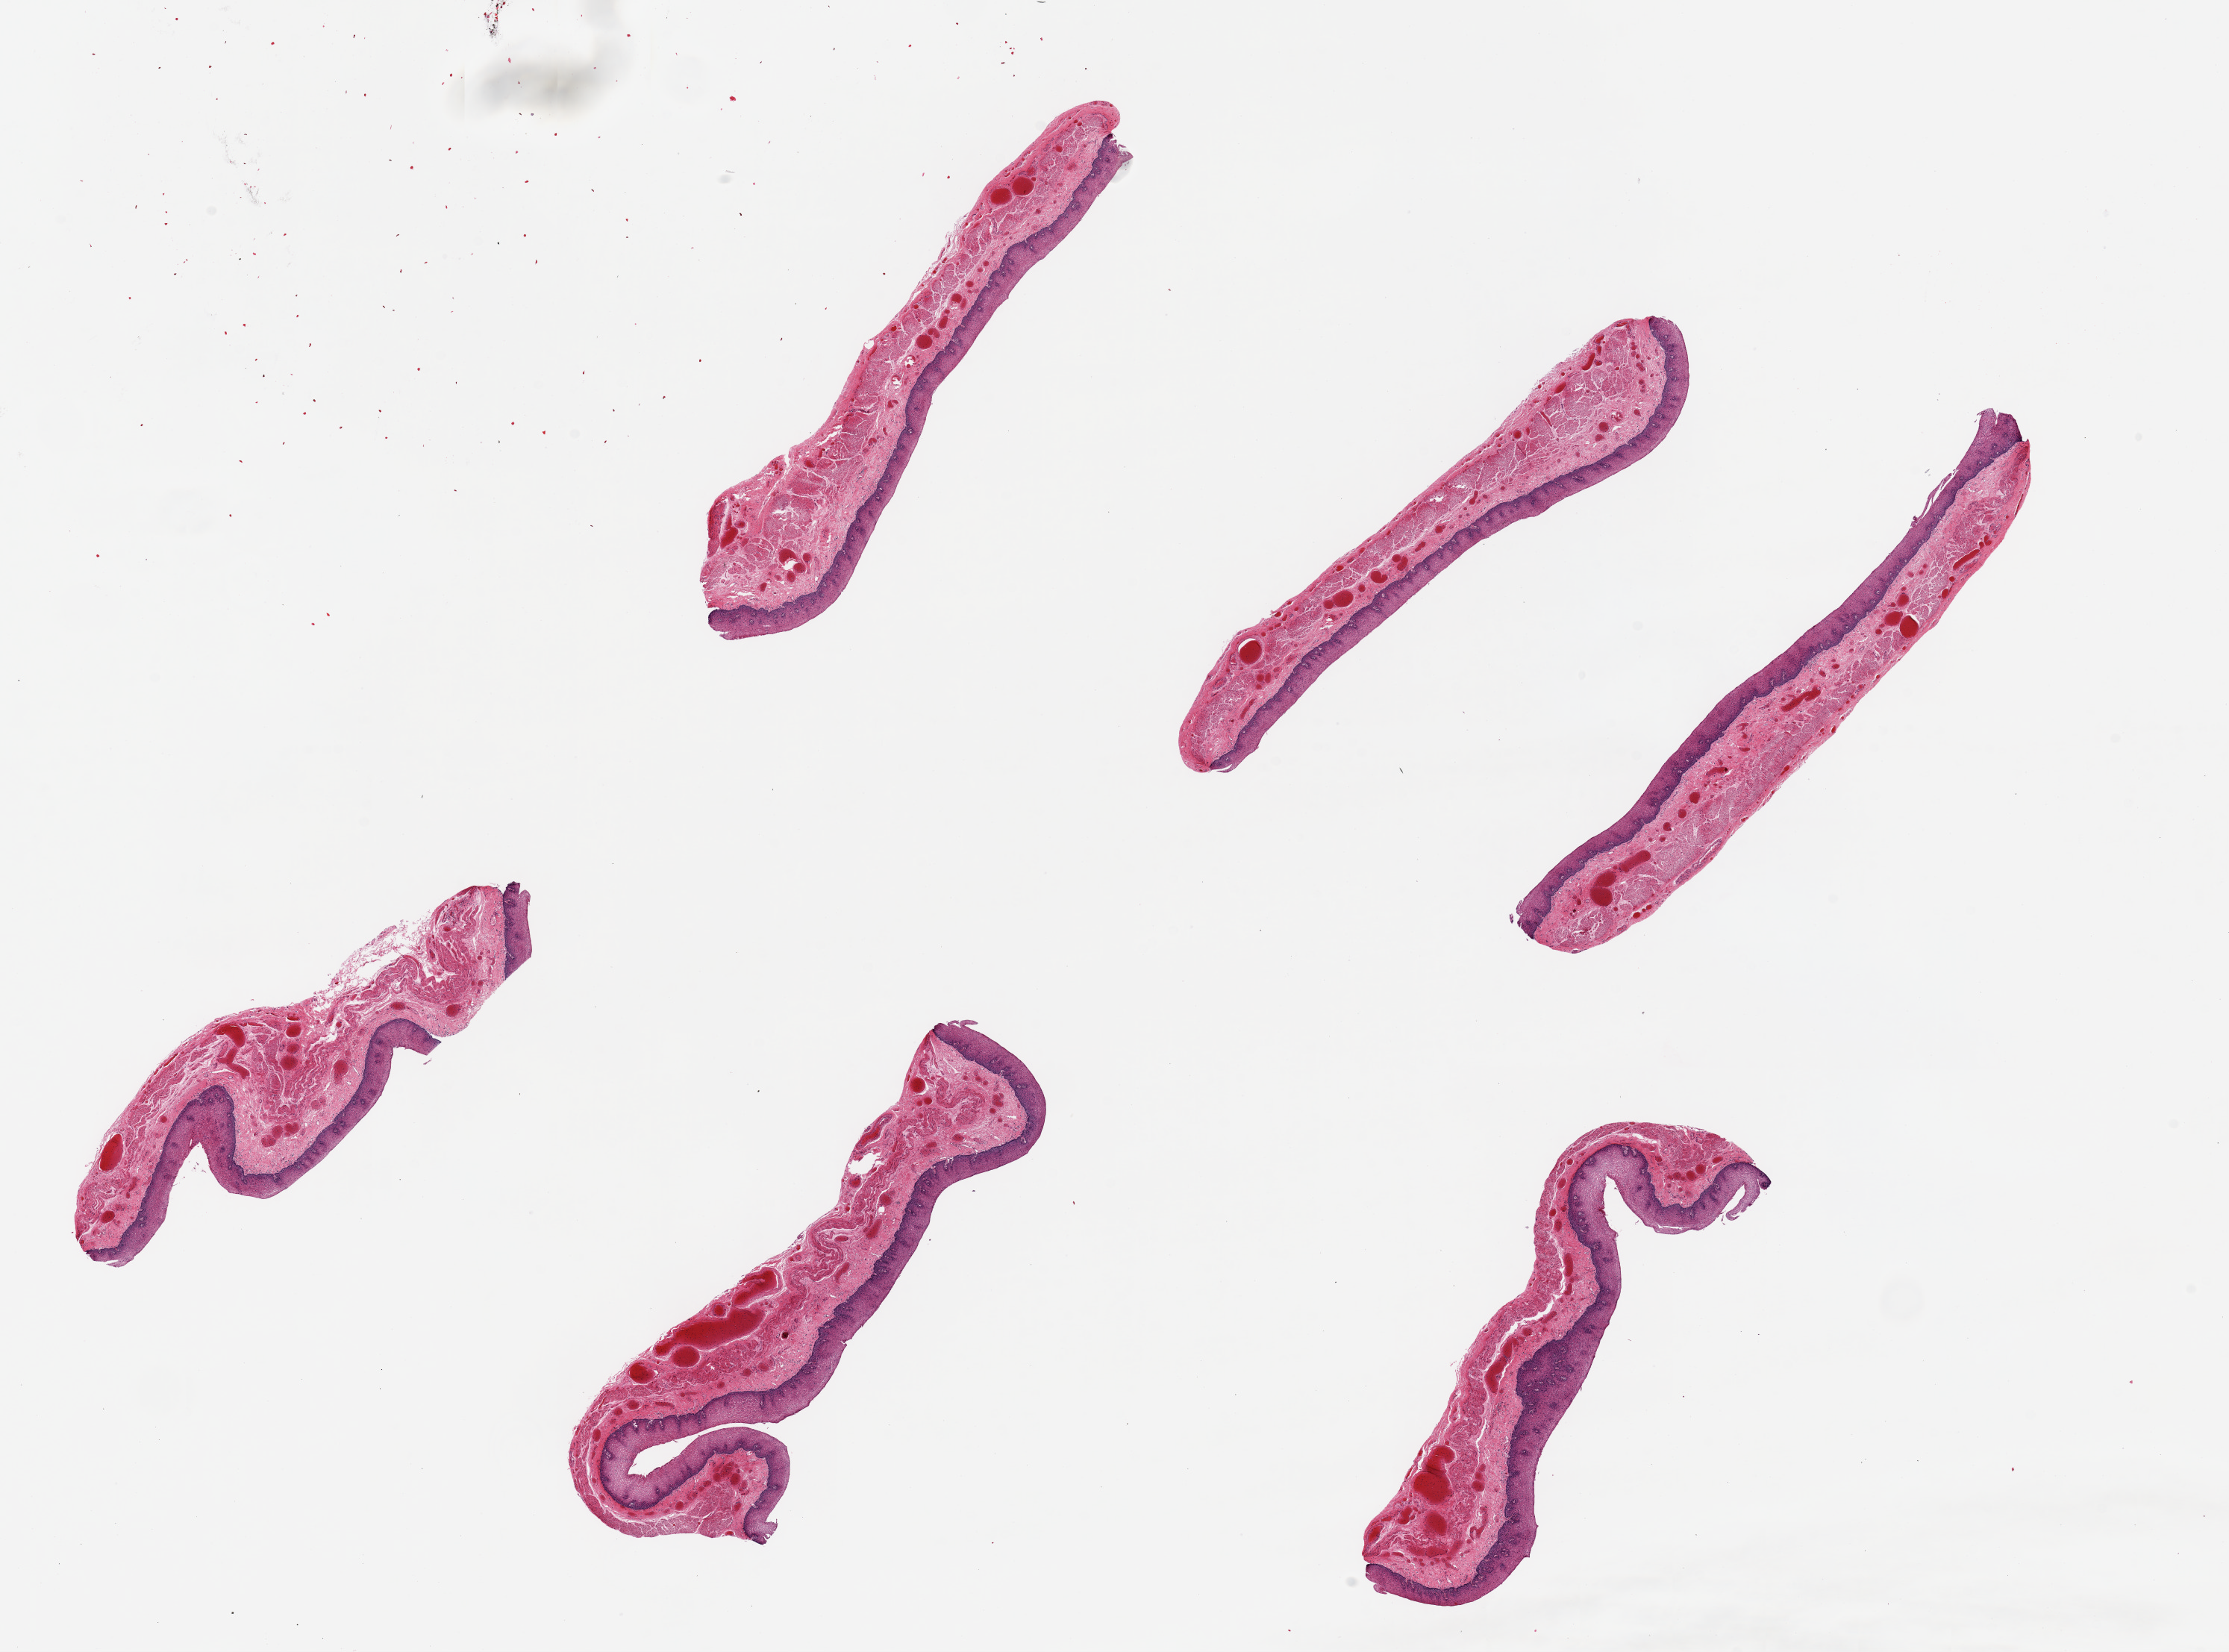
Hematoxylin and eosin (H&E) whole-slide image, brightfield, whole scanned area (about 23.6 x 17.5 mm, slide scanned at 20x) shown as a low-resolution overview, PAXgene-fixed paraffin-embedded (PFPE) section, section of esophageal mucous membrane (target tissue), donor tissue sample. Donor: female.
Reviewer comment on this tissue sample: 6 pieces~7x1mm; squamous mucosa is ~10-20% of thickness.